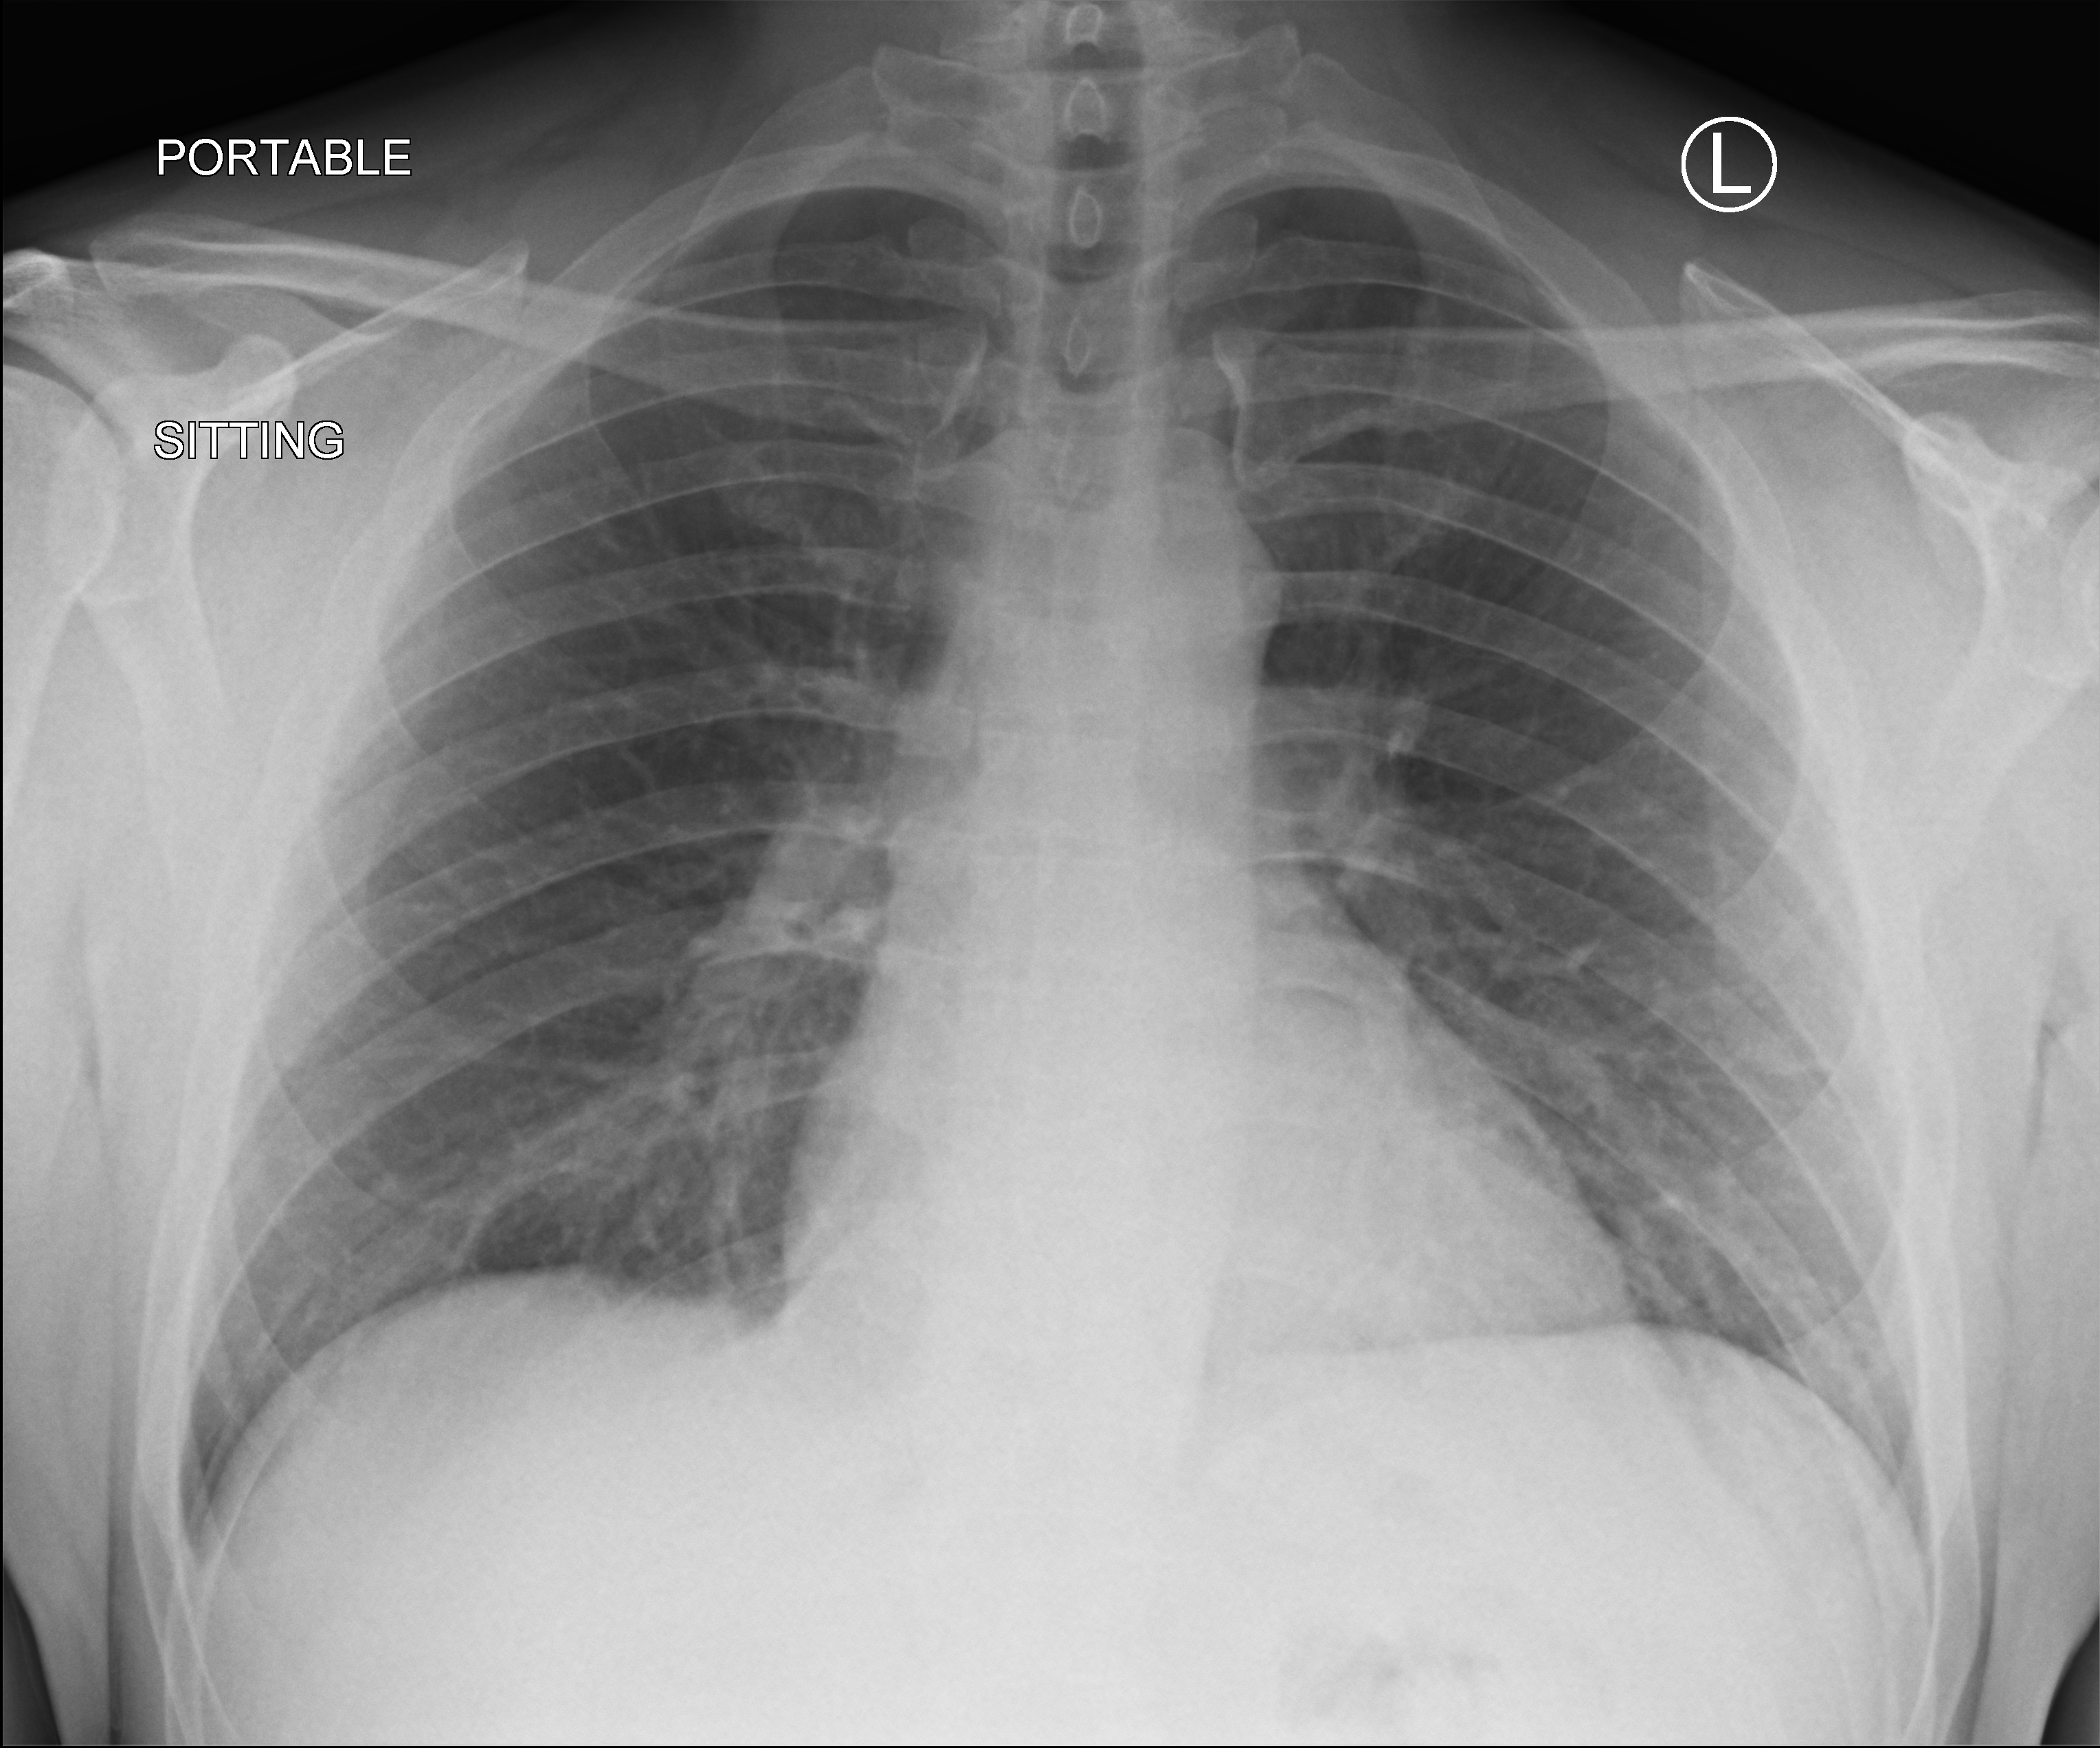
Portable chest radiograph, anteroposterior (AP) projection. Patient hospitalised with COVID-19; male, aged 18–59 years.
Hospital-stay facts (about this admission, not read from this image; timing relative to this image not recorded): diabetes (admission record): no; mechanically ventilated during this hospital stay: no.